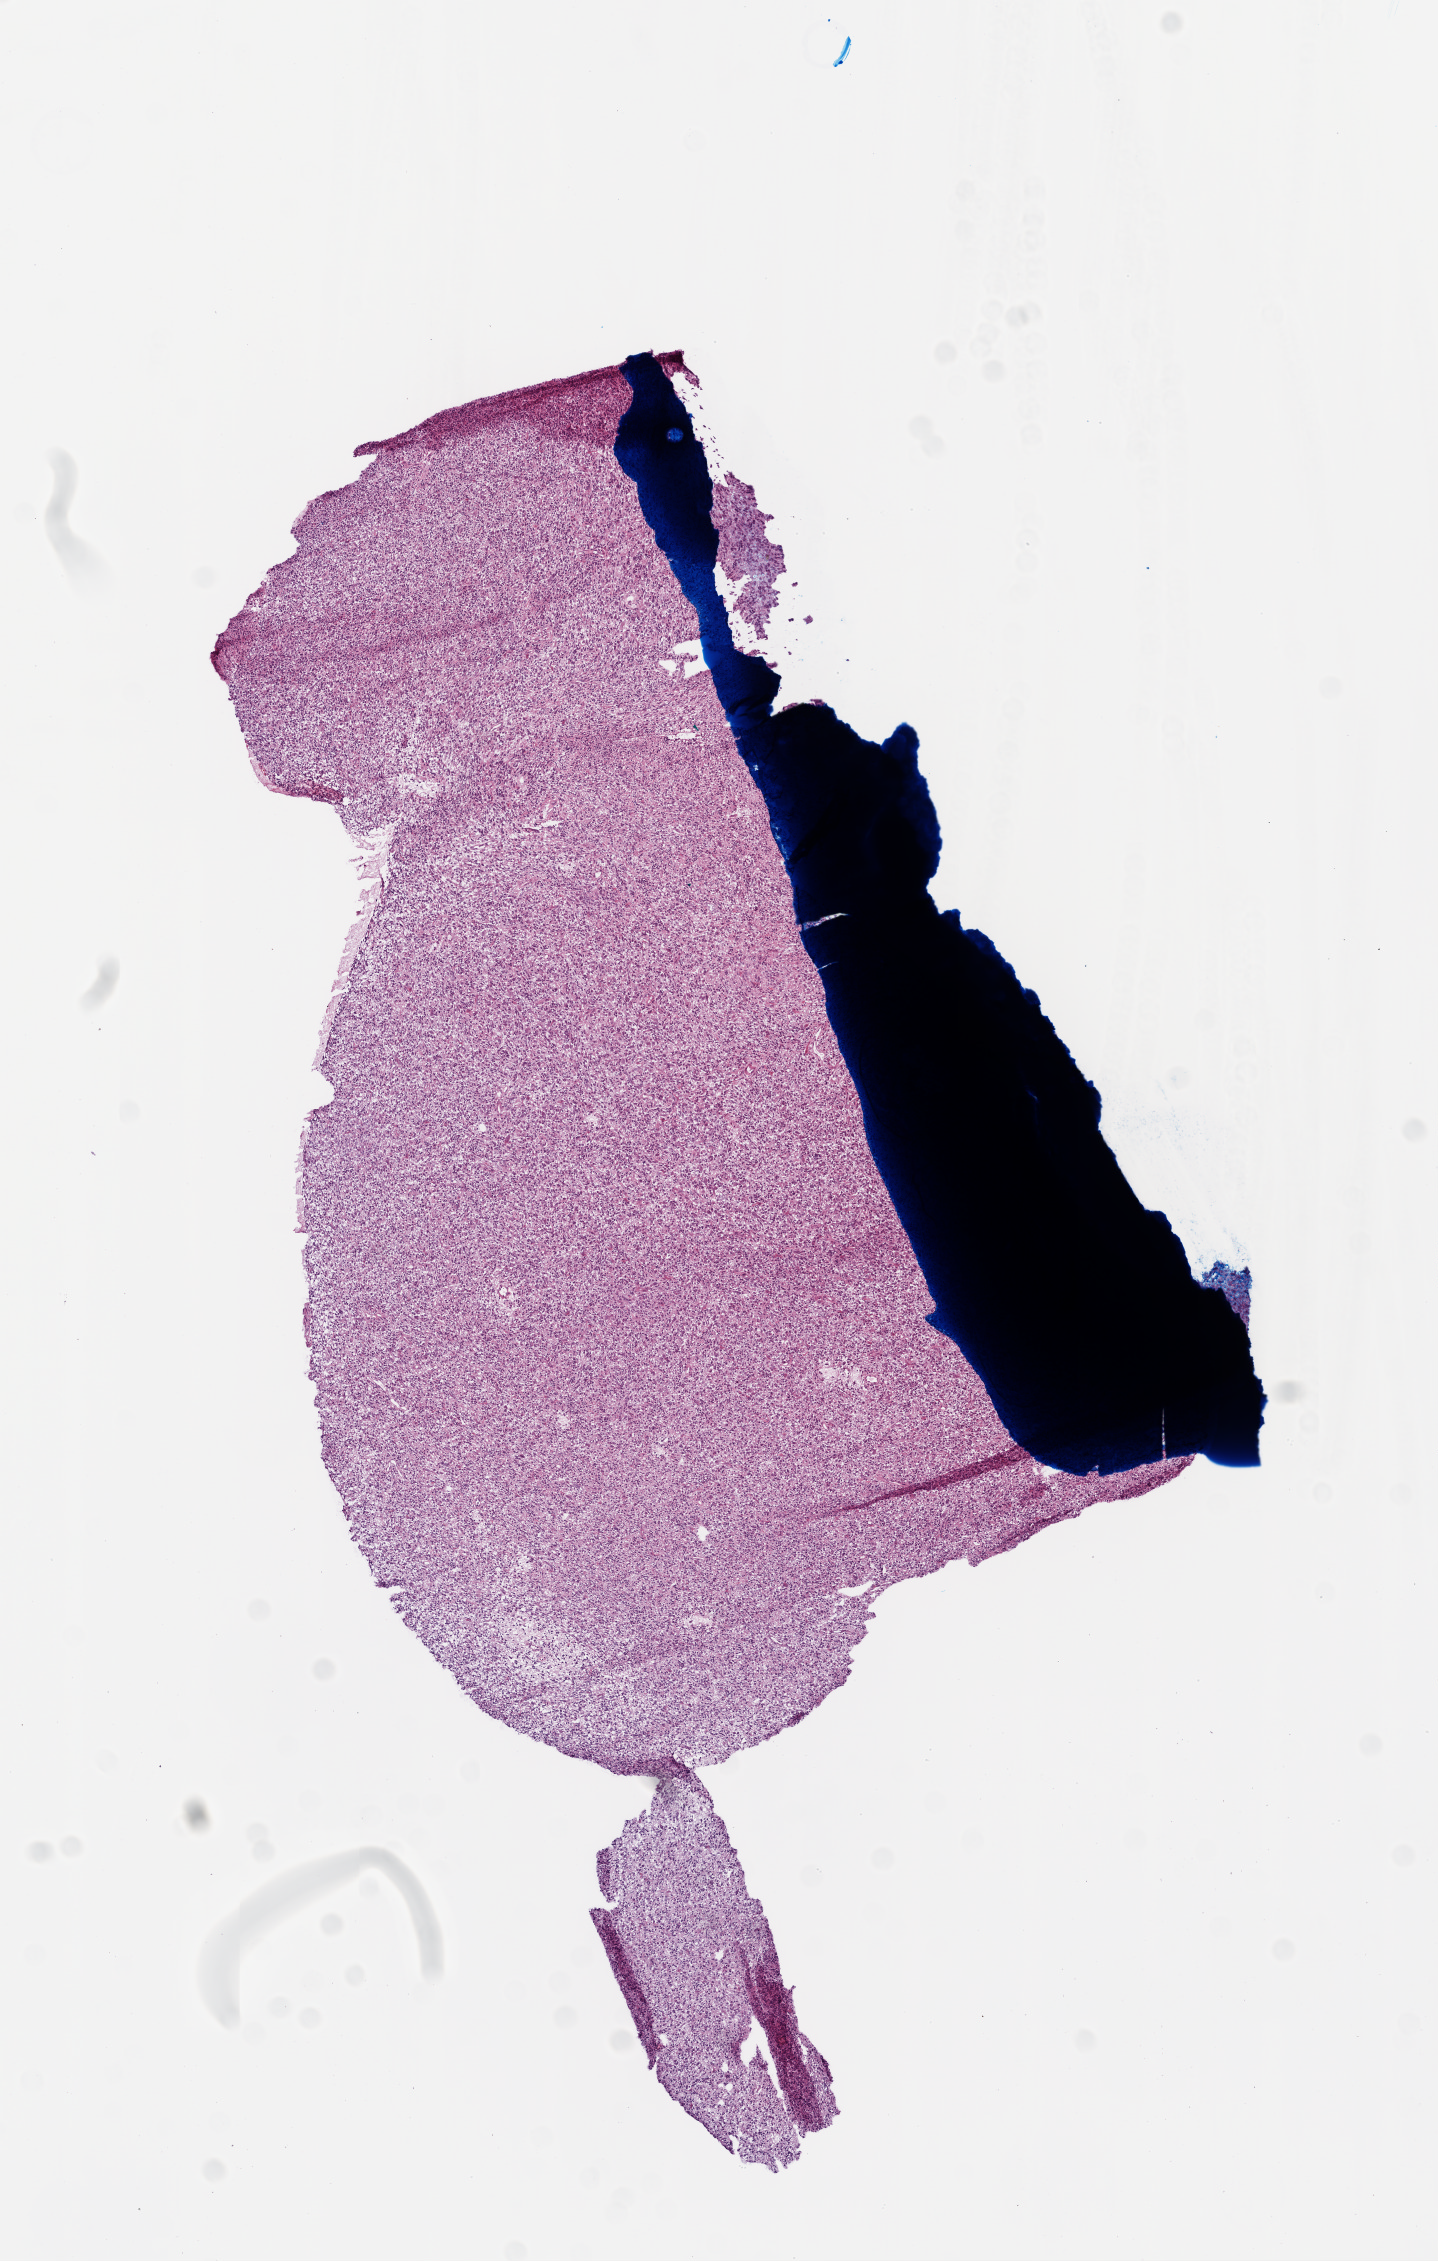
Digitized Hematoxylin and eosin (H&E) stained tissue section (whole slide), whole scanned area (about 5.8 x 9.1 mm) shown as a low-resolution overview. Frozen section from the top of the tissue portion. Primary tumour sample from the brain. Patient: male, age at initial diagnosis 53 years.
Diagnosis: Glioblastoma.